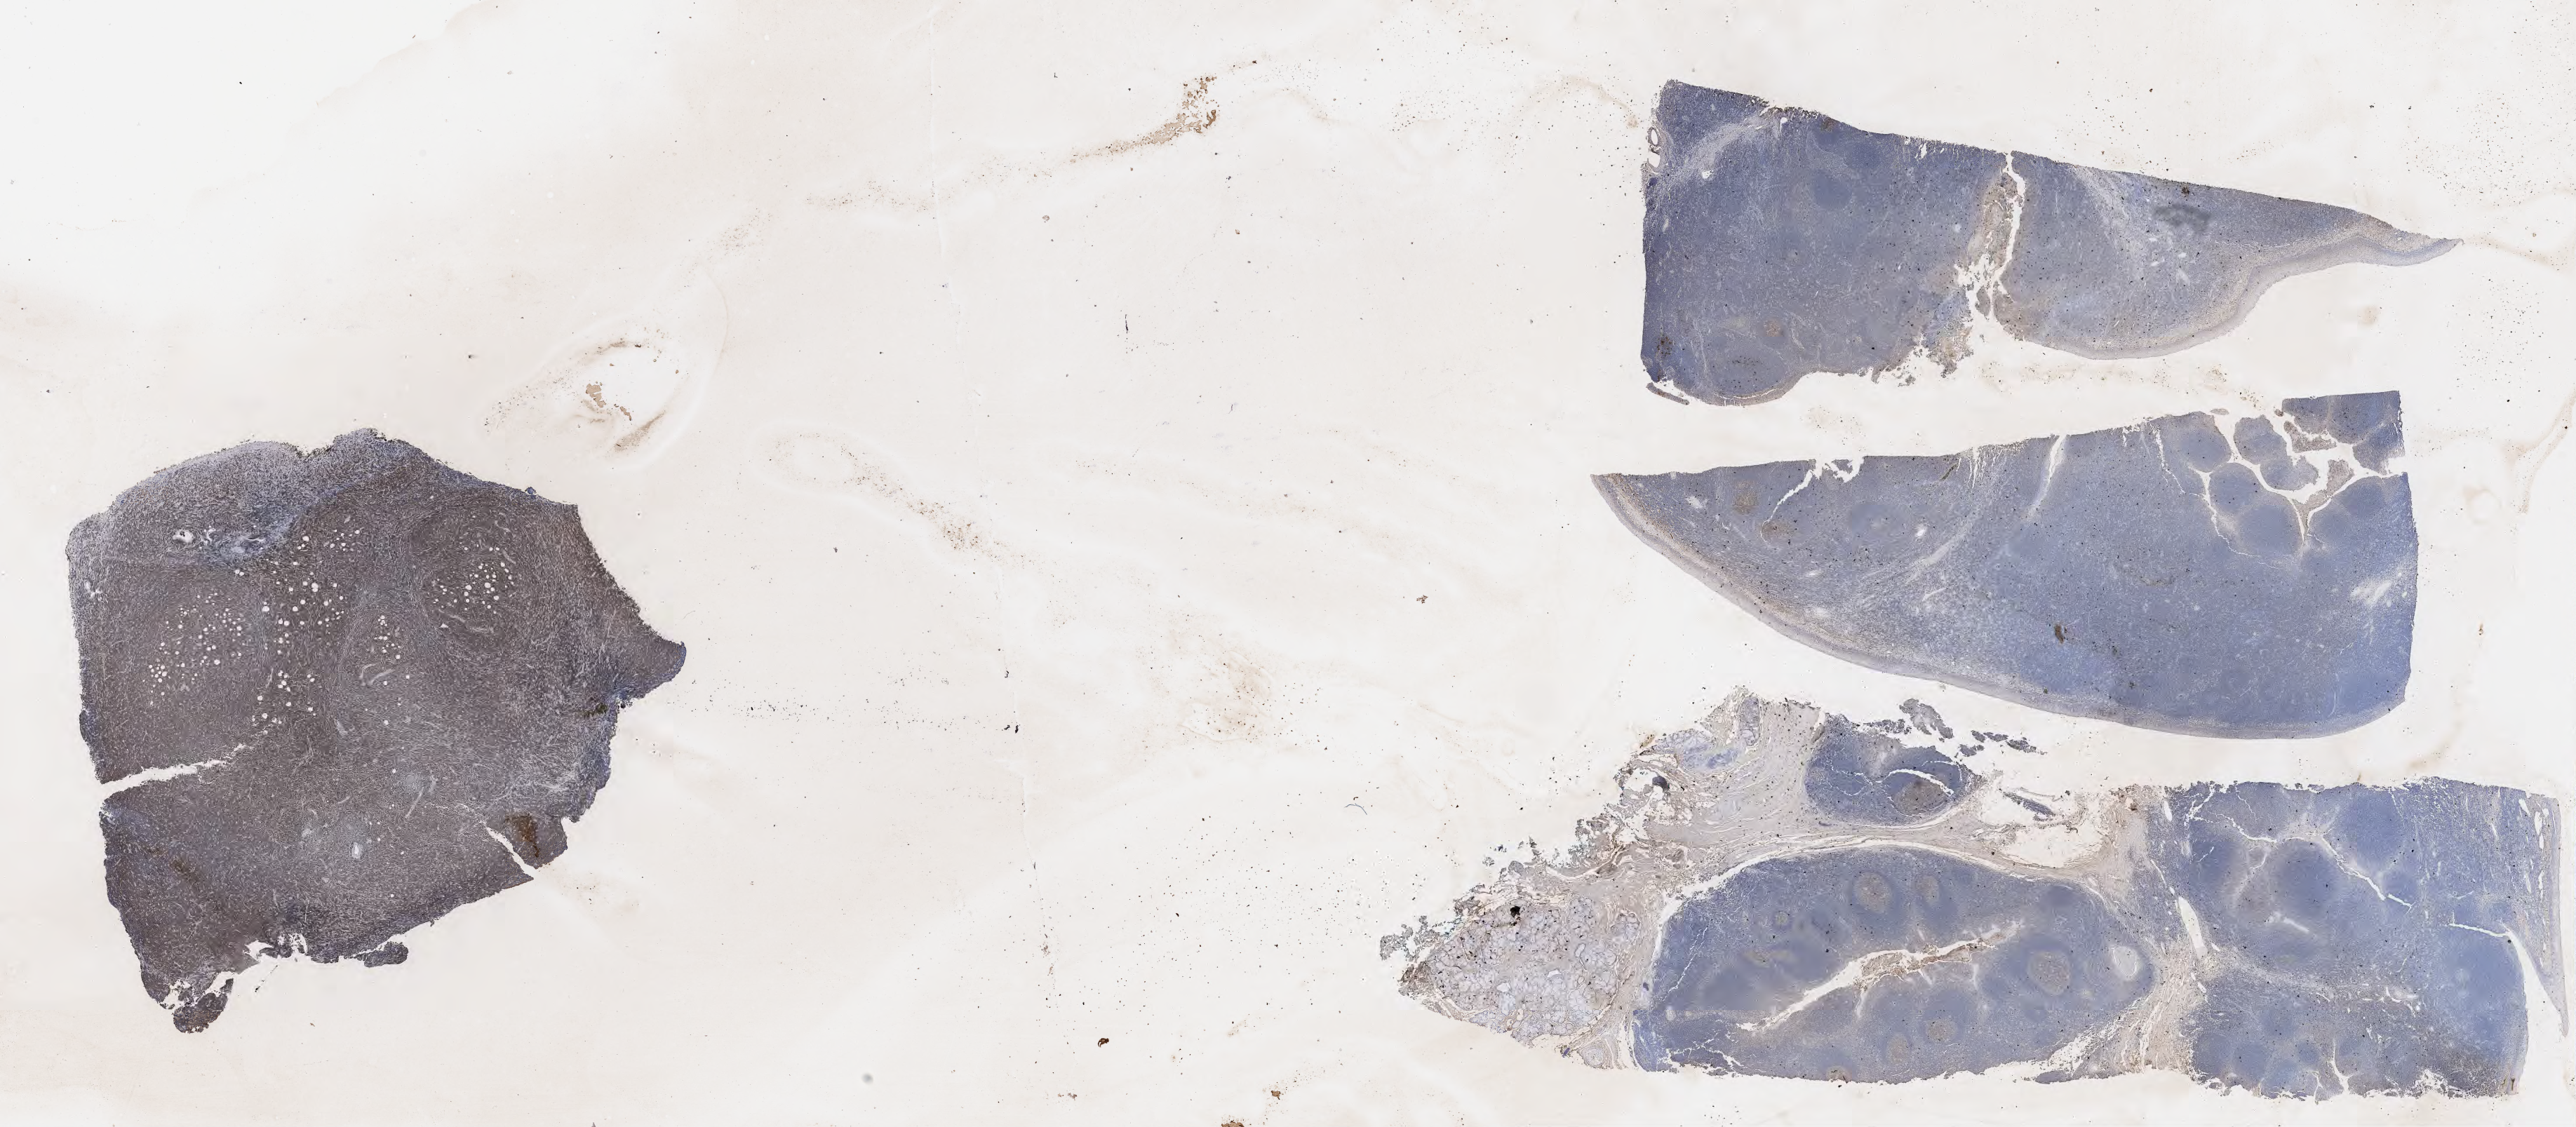
IHC for CD10, whole-slide image — a low-resolution overview of the entire scanned area, about 29.7 x 13.0 mm, tumor tissue, anatomic site: retroperitoneum. Patient: male, age at initial diagnosis 7 years.
Histologic diagnosis: Diffuse large B-cell lymphoma, NOS.